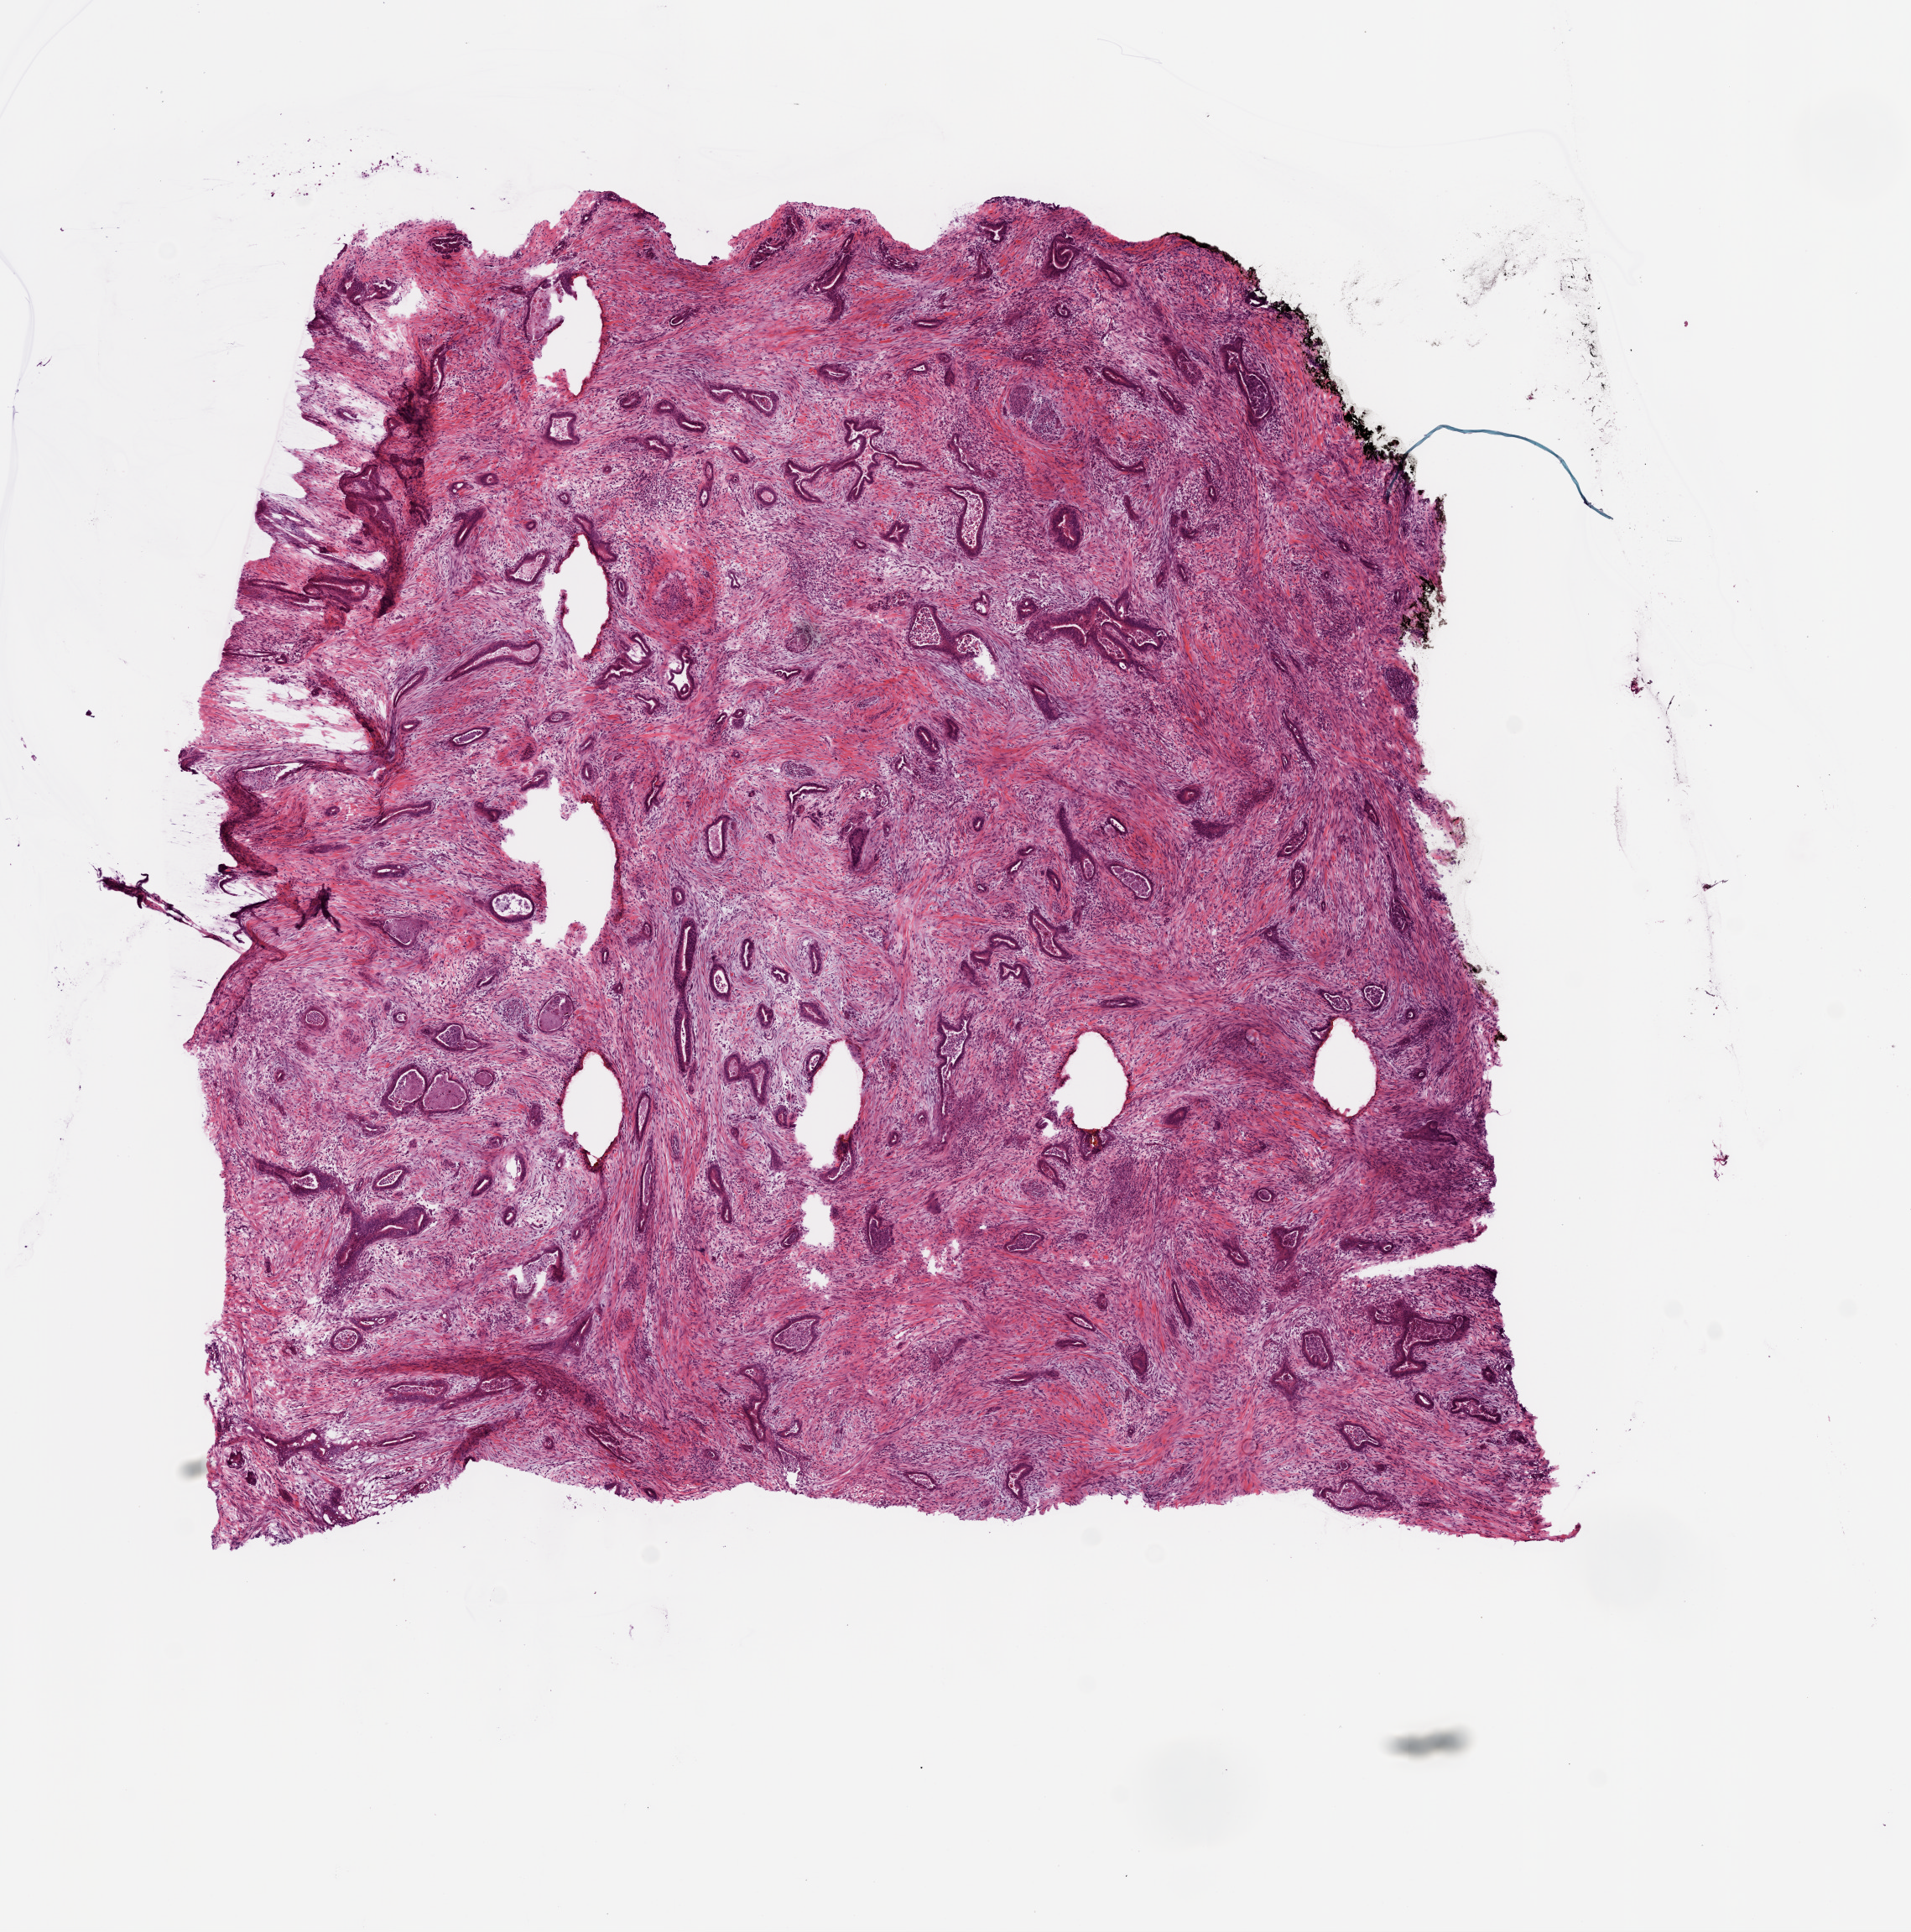
Digitized H&E tissue section (whole slide) — low-resolution overview of the scanned area, about 9.2 x 9.3 mm. Frozen section. Primary tumour sample from the pancreas. Patient: male, age at initial diagnosis 66 years.
Diagnosis: Infiltrating duct carcinoma, NOS (head of pancreas).